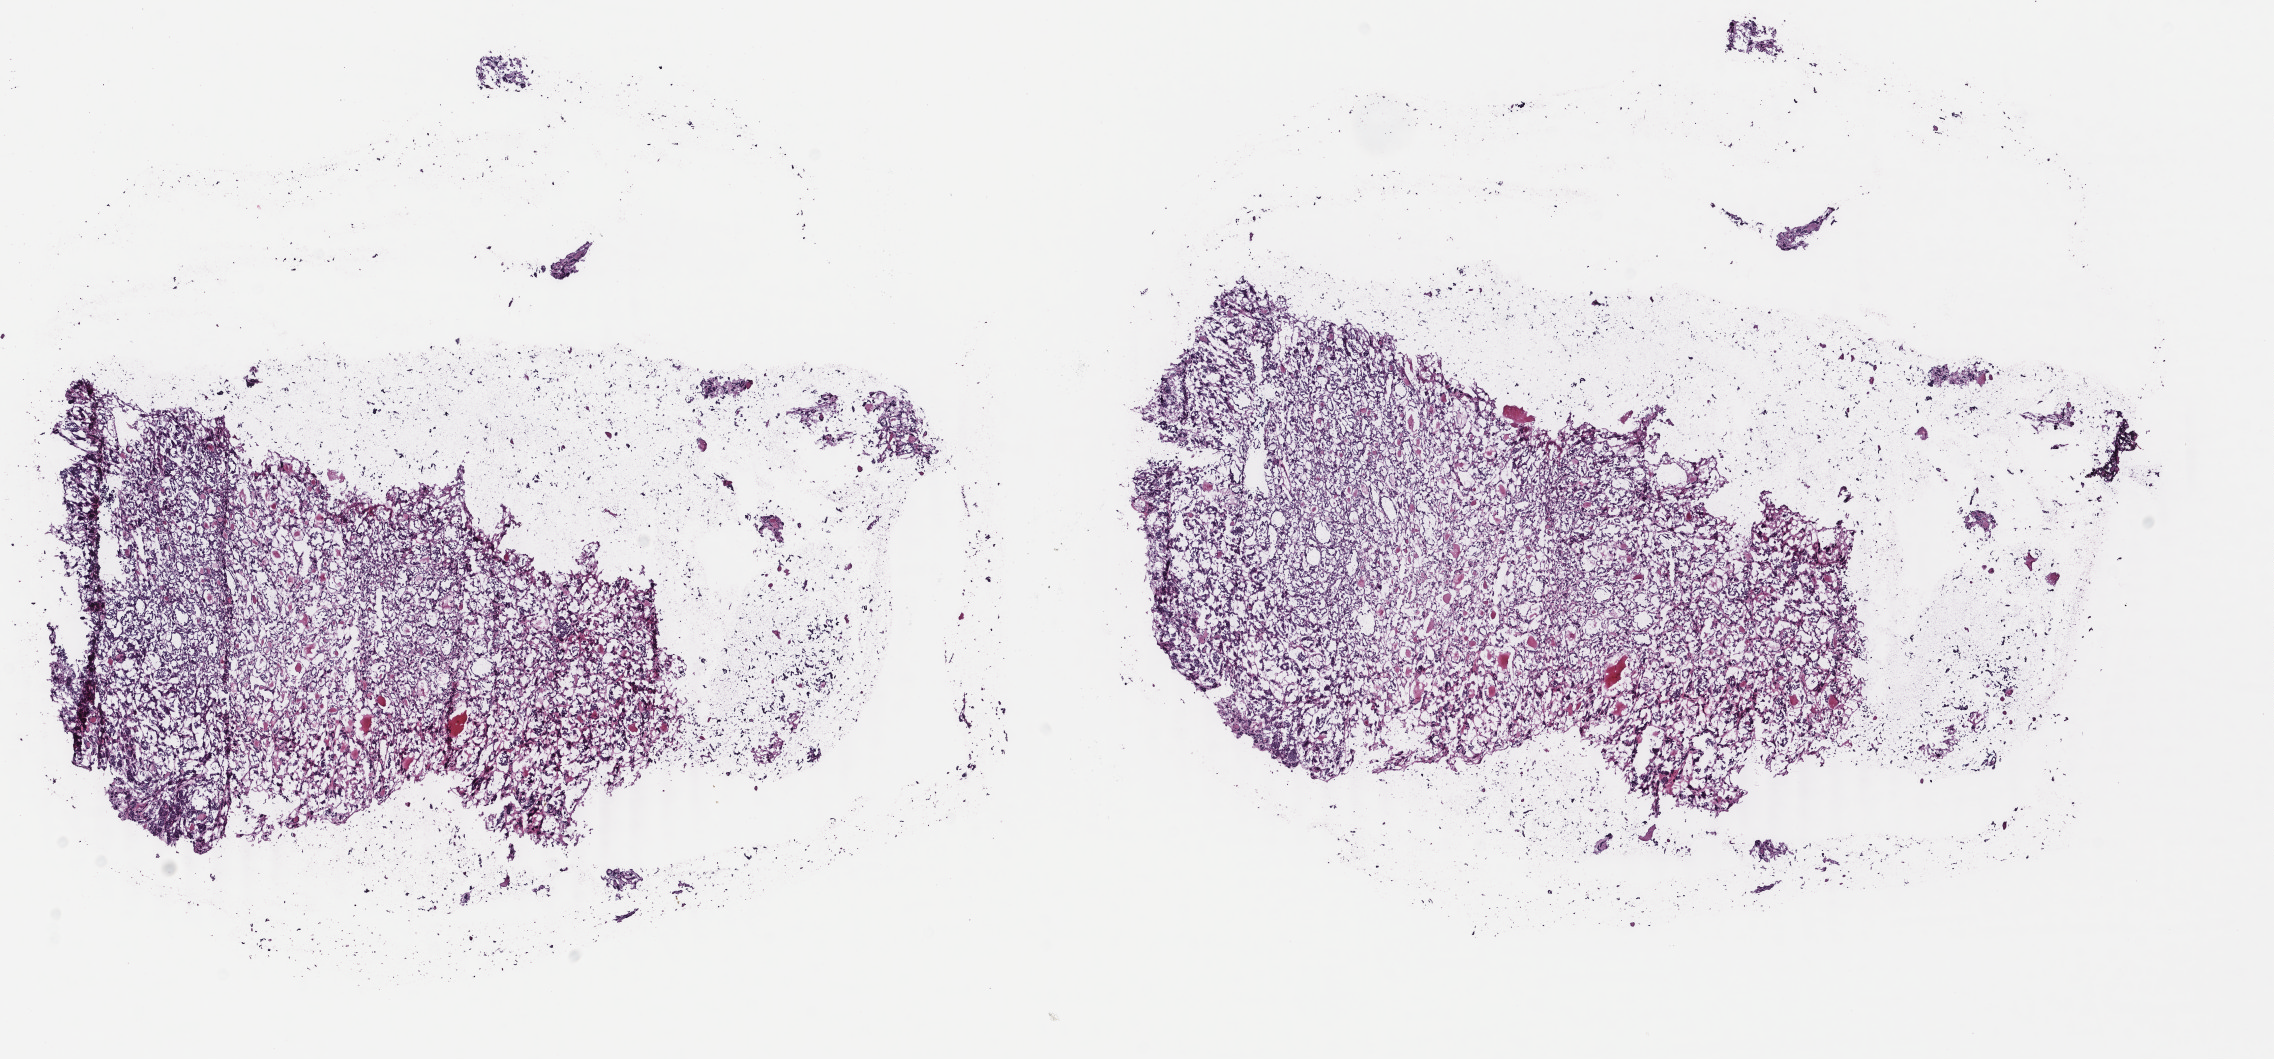
Hematoxylin and eosin (H&E) stained whole-slide image, shown as a low-resolution overview of the whole scanned area (about 18.1 x 8.4 mm). Frozen section from the top of the tissue portion. Thyroid, primary tumour sample. Female, age 45 years at initial diagnosis. Composition of this section per pathologist review: tumour cells 100%, tumour nuclei 98%, normal cells 0%, stromal cells 0%, necrosis 0%. Infiltration values recorded for this section: lymphocyte infiltration 0%, monocyte infiltration 0%, neutrophil infiltration 0%.
AJCC pathologic stage: I (7th edition). Laterality: left. Lymph nodes positive (case pathology): 0 of 3 examined. TNM: T1b N0 M0. Pathologic diagnosis: Papillary carcinoma, follicular variant.